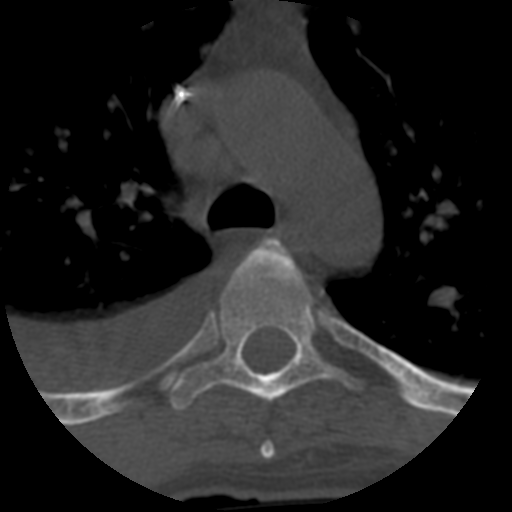
CT including the spine, one axial slice; position 457 of 708 along the scan axis; reconstruction kernel STANDARD; 120 kVp; one of 3 acquisitions stored at this slice position; bone window (W 1800 / L 400 HU); 1.25 mm slice thickness; 512 × 512 image matrix. Patient age 55 years. From the clinical record (not read from this slice): primary cancer: colon; vertebrae with lytic lesions (as recorded): T12, L1, L5.
Annotated regions visible in this slice (semi-automatically segmented with operator editing):
- T4 vertebra: bounding box <260,442,276,459> (left, top, right, bottom; pixels)
- T5 vertebra: <170,237,365,408>